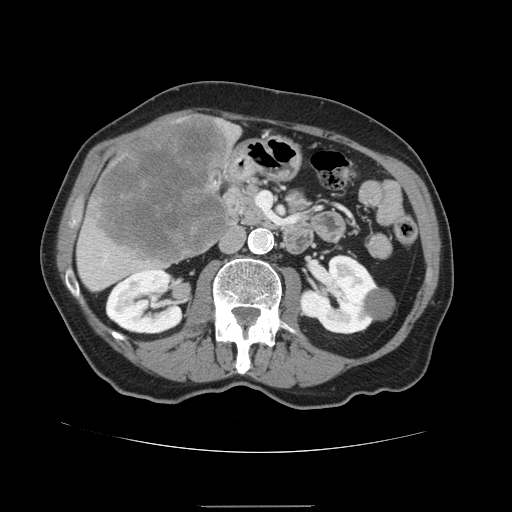
Contrast-enhanced abdominal CT, one axial slice. Position 58 of 168 along the scan axis. 120 kVp. Soft-tissue window (W 400 / L 40 HU). 512 × 512 image matrix, field of view 386 × 386 mm. Male patient, age 74 years. Case-level facts recorded for this patient, not image findings: diagnosis: colorectal cancer liver metastases, imaged before liver resection; multiple liver metastases: no; largest metastasis: 14.5 cm; disease in both lobes: yes.
Outlined on this slice (outlined manually by an expert reader):
- liver: box from (x=76, y=113) to (x=242, y=293) px
- liver metastasis: (x=96, y=118)–(x=231, y=265)